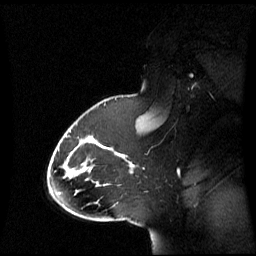
Breast MRI (dynamic contrast-enhanced), one sagittal slice. Position 43 of 60 along the scan axis. Dynamic contrast-enhanced series, image 2 of 3 at this slice position (ordered by acquisition). 1.5 T. TE 4.2 ms, TR 8.4 ms. 2.8 mm slice thickness. 256 × 256 image matrix, field of view 270 × 270 mm. Female patient, age 43 years. From the clinical record (not read from this slice): setting: breast cancer imaged before/during neoadjuvant chemotherapy; receptor status: triple-negative.
Outlined on this slice (semi-automatically segmented with operator editing):
- analysis volume of interest (the breast-tissue region the enhancement analysis was run in; not a lesion): bounding box <65,118,143,198> (left, top, right, bottom; pixels)
- tumour enhancement mask (voxels above the 70 % enhancement threshold inside the analysis volume of interest): <112,151,135,167>